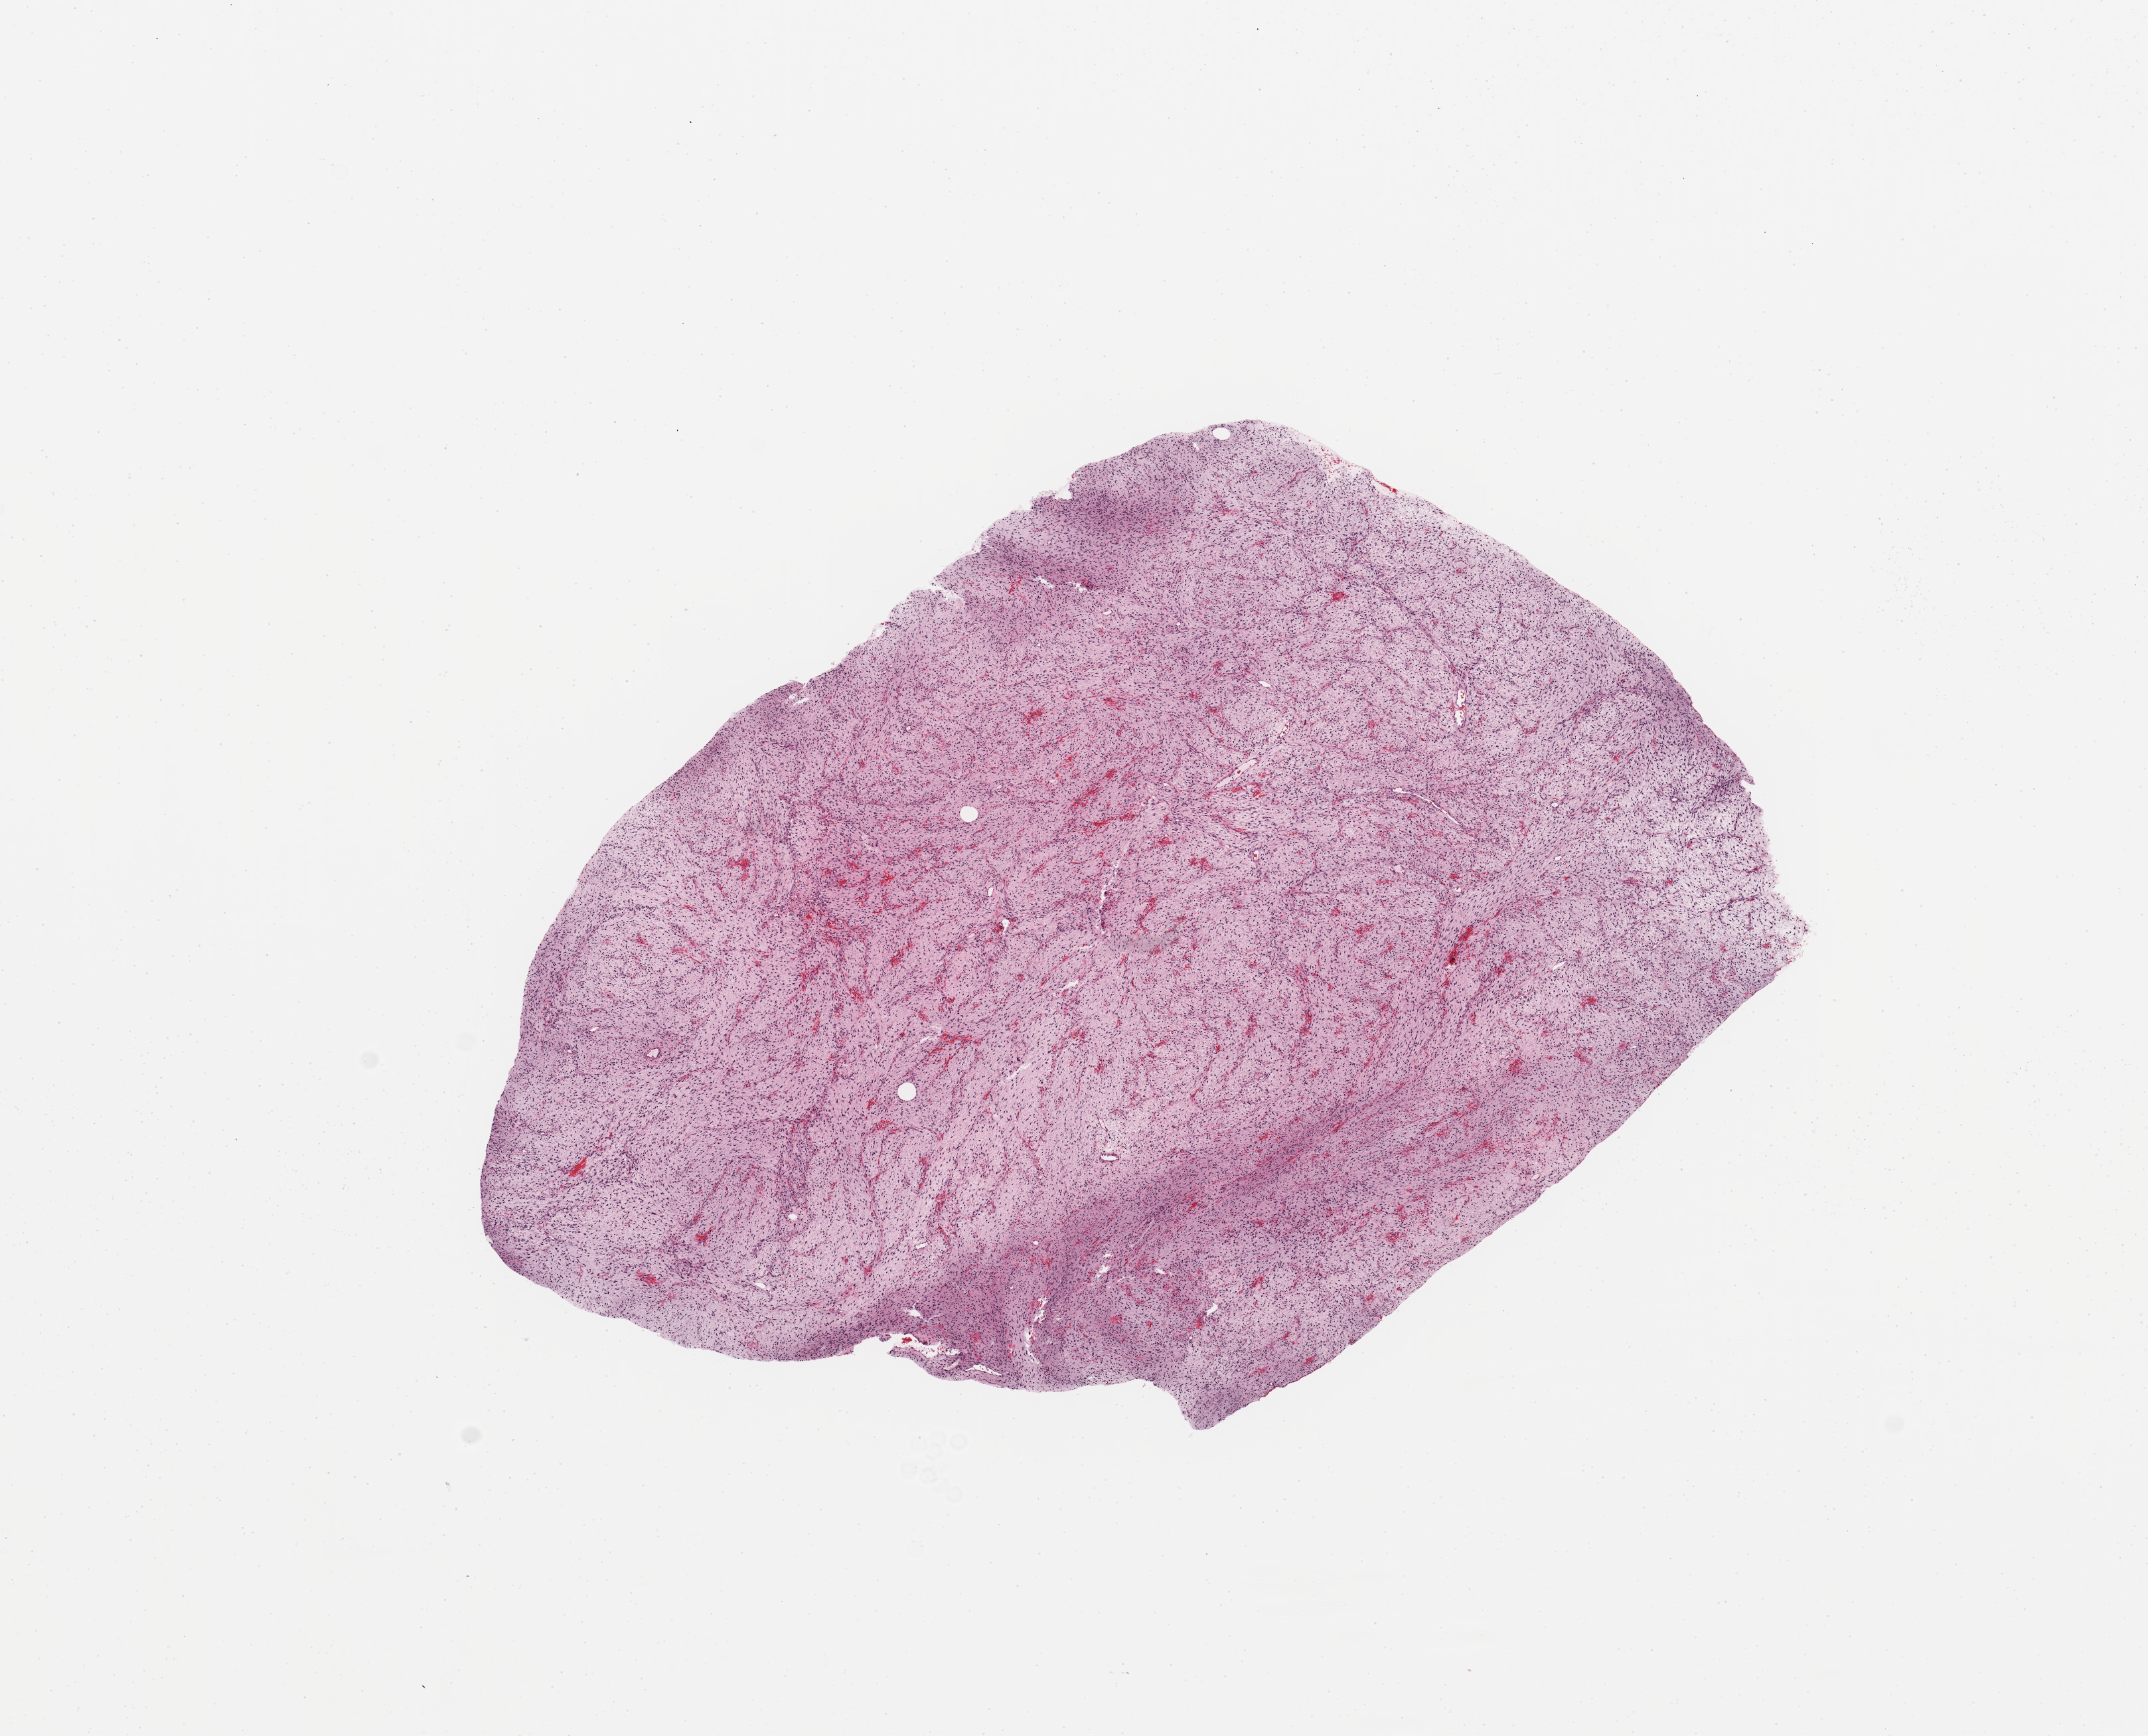
Digitized Hematoxylin and eosin (H&E) stained tissue section (whole slide) — low-resolution overview of the scanned area, about 12.8 x 10.3 mm (from a 20x scan); tumour tissue sample. Patient sex: male.
Patient diagnosis (cohort enrolment): sarcoma (site not recorded at cohort level).